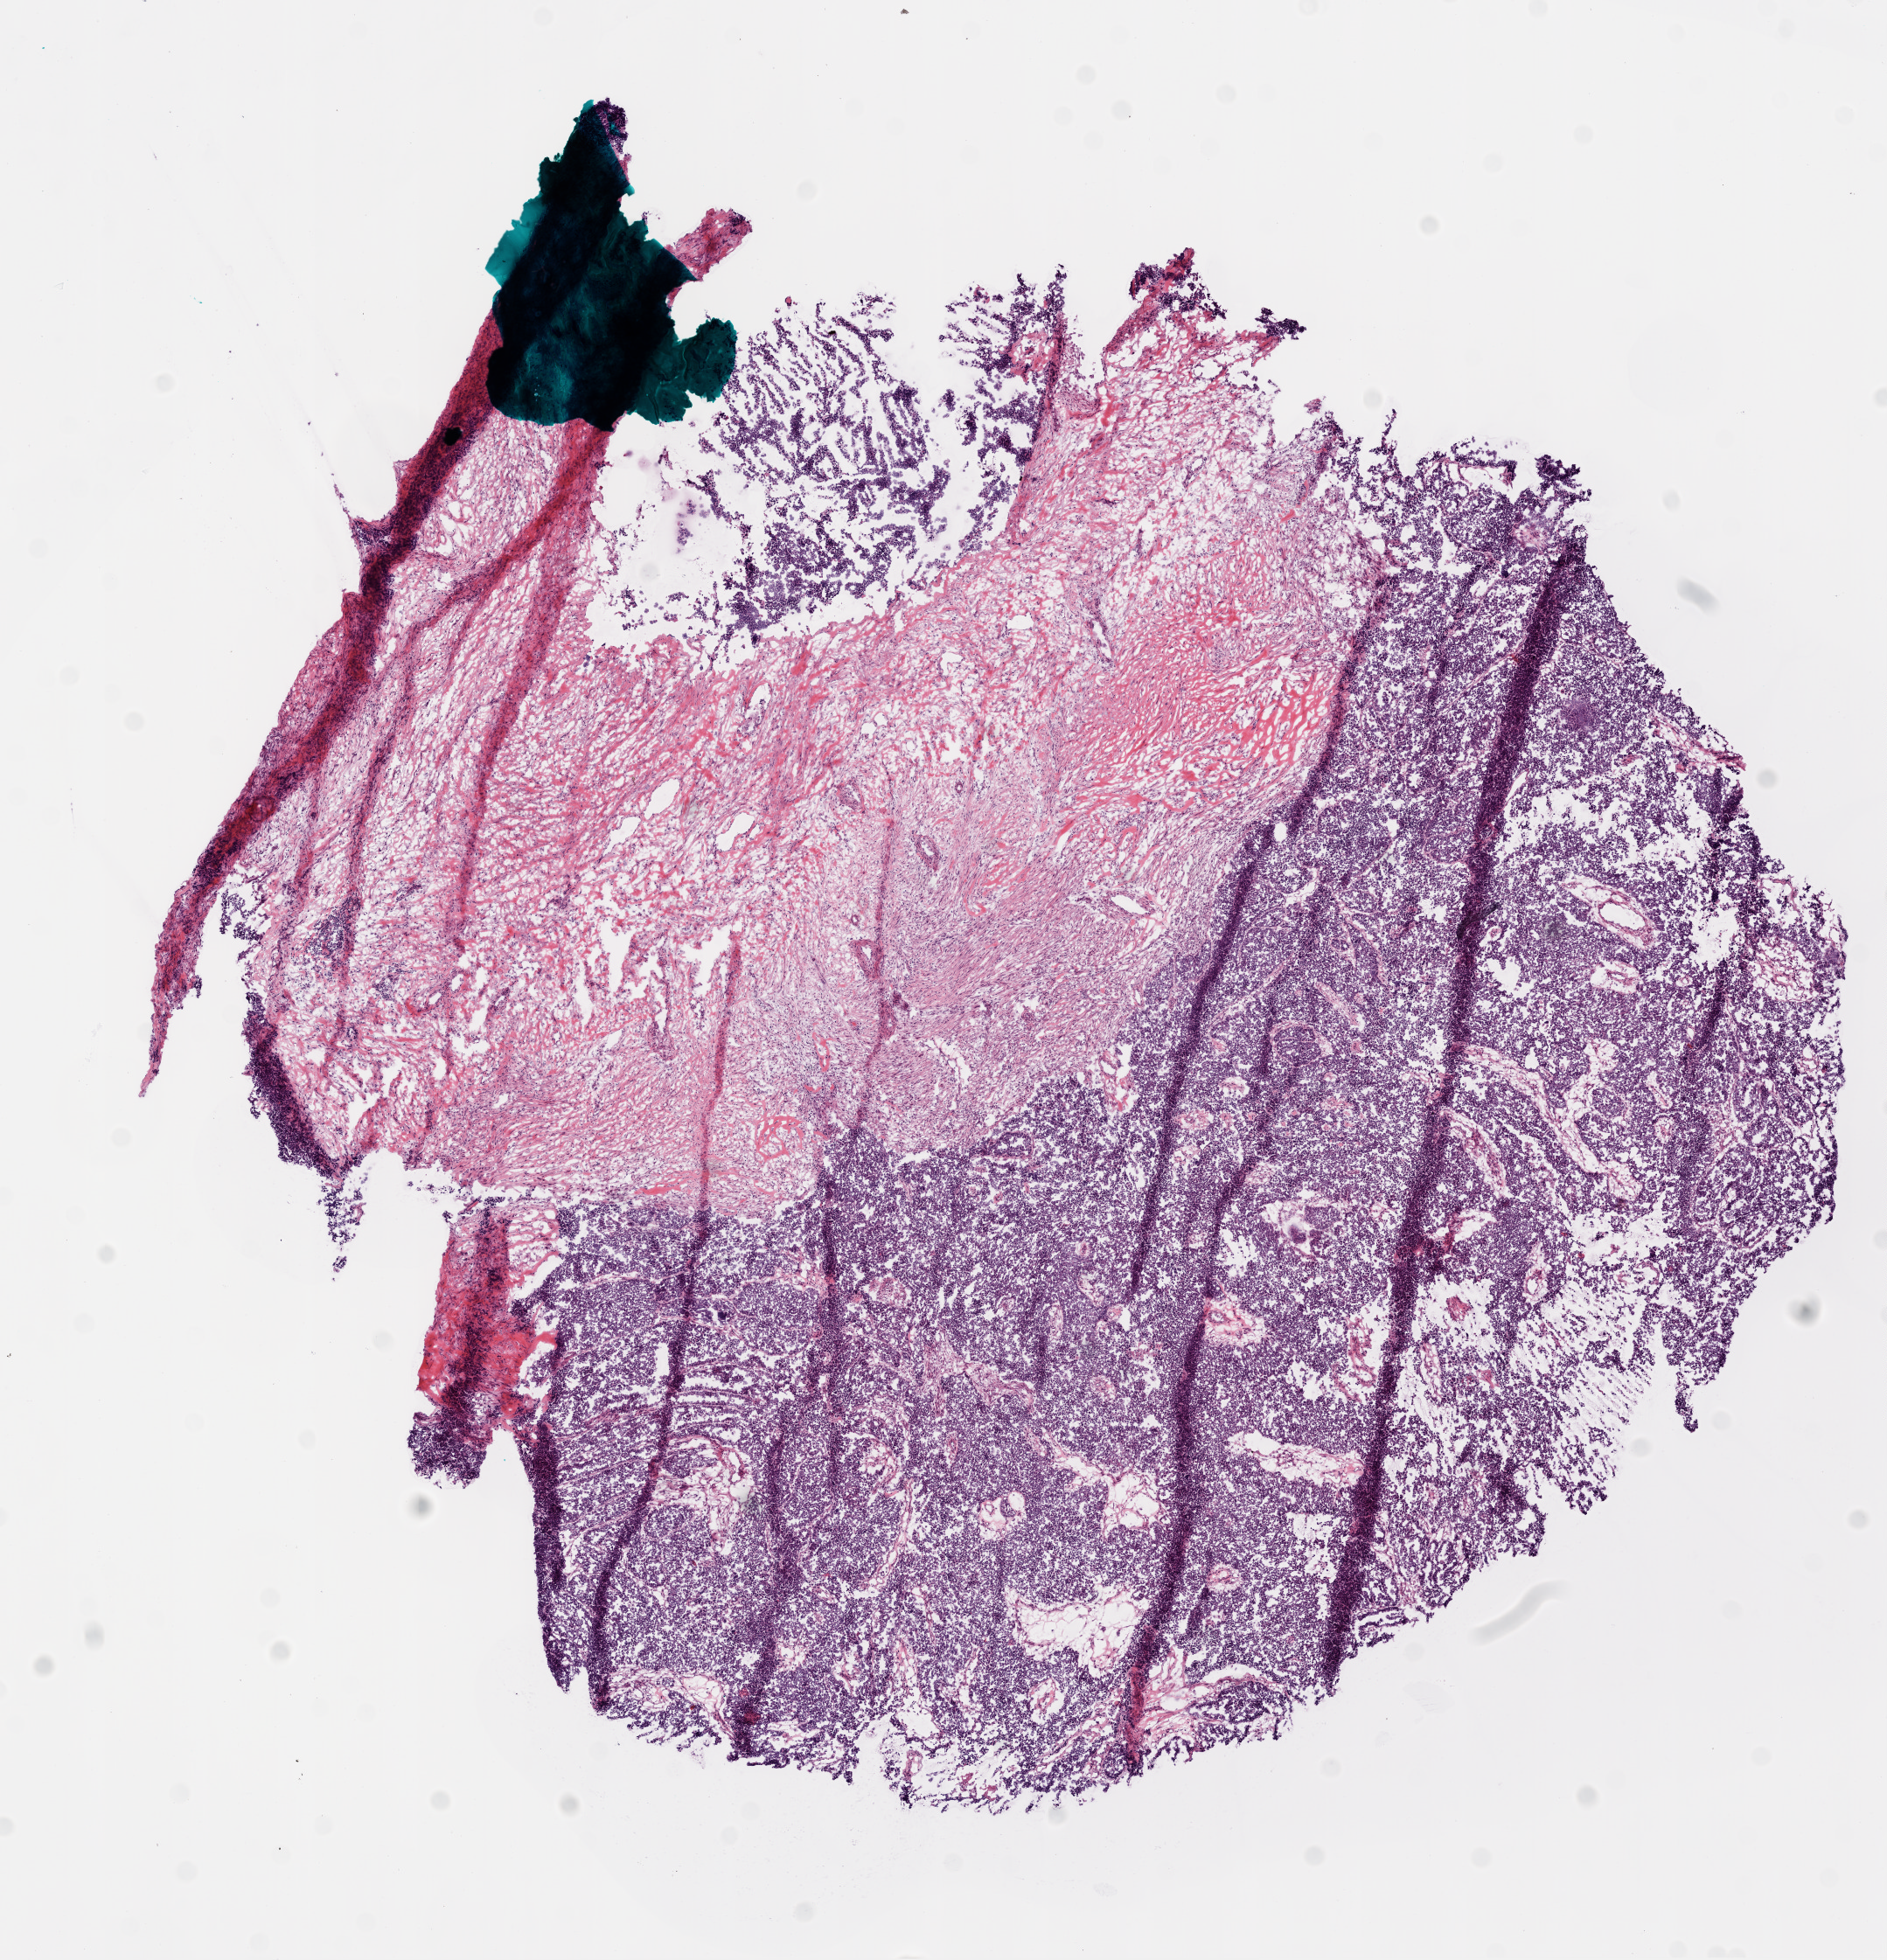
Whole-slide histology image, H&E-stained — whole scanned area (about 8.7 x 9.0 mm) shown as a low-resolution overview. Frozen section from the bottom of the tissue portion. Primary tumour sample from the ovary. Female, age 62 years at initial diagnosis. Histologic grade: G3 (poorly differentiated). Pathologist review of this section (percent, as recorded): tumour nuclei 90%, normal cells 0%, necrosis 0%.
• pathologic diagnosis: Serous cystadenocarcinoma, NOS
• FIGO stage: IIIC